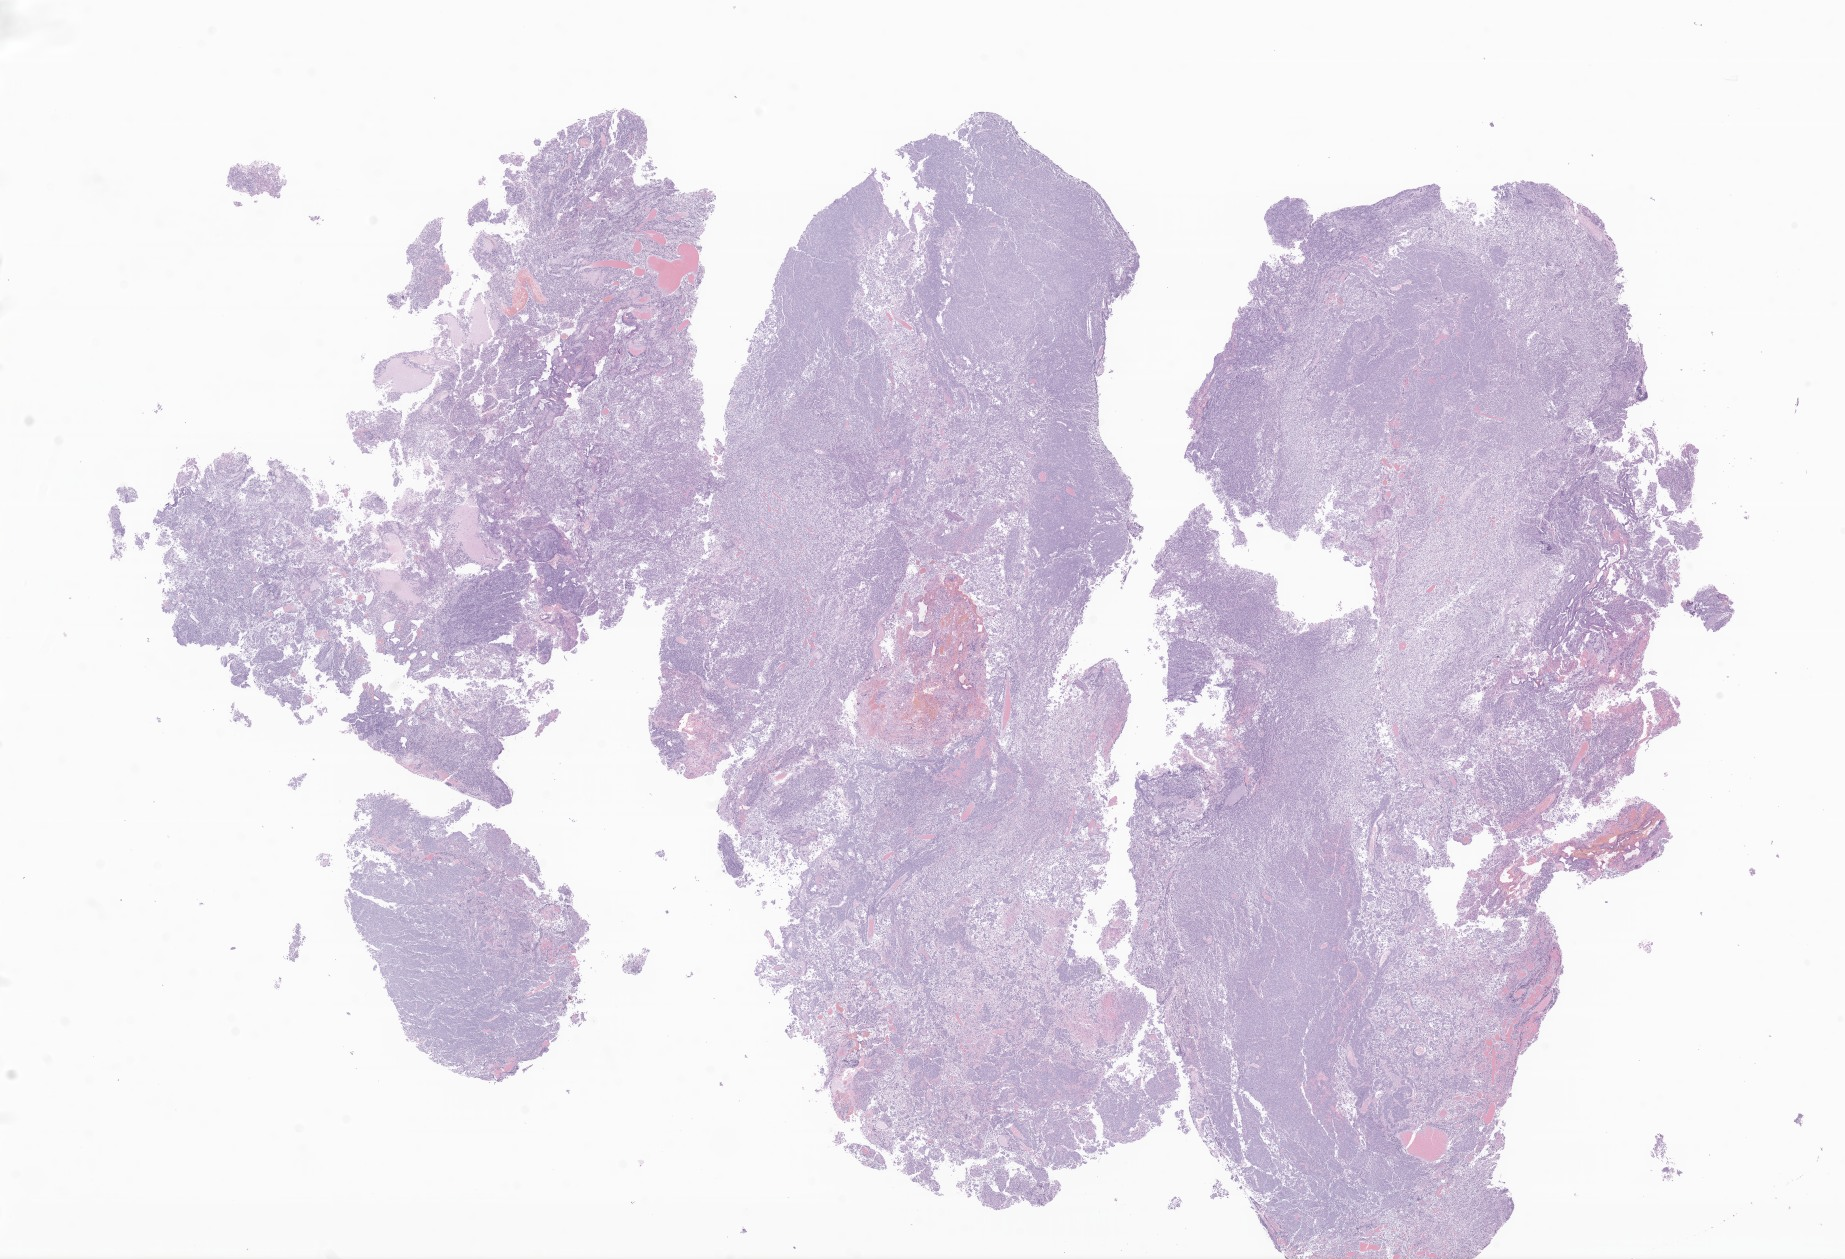
Whole-slide image, hematoxylin and eosin (H&E) stain of tumor tissue from the cerebellum — low-resolution overview of the scanned area, about 31.1 x 21.2 mm, FFPE section. Patient: male, age 100 months (8 years 4 months).
Diagnosis: Medulloblastoma, NOS.